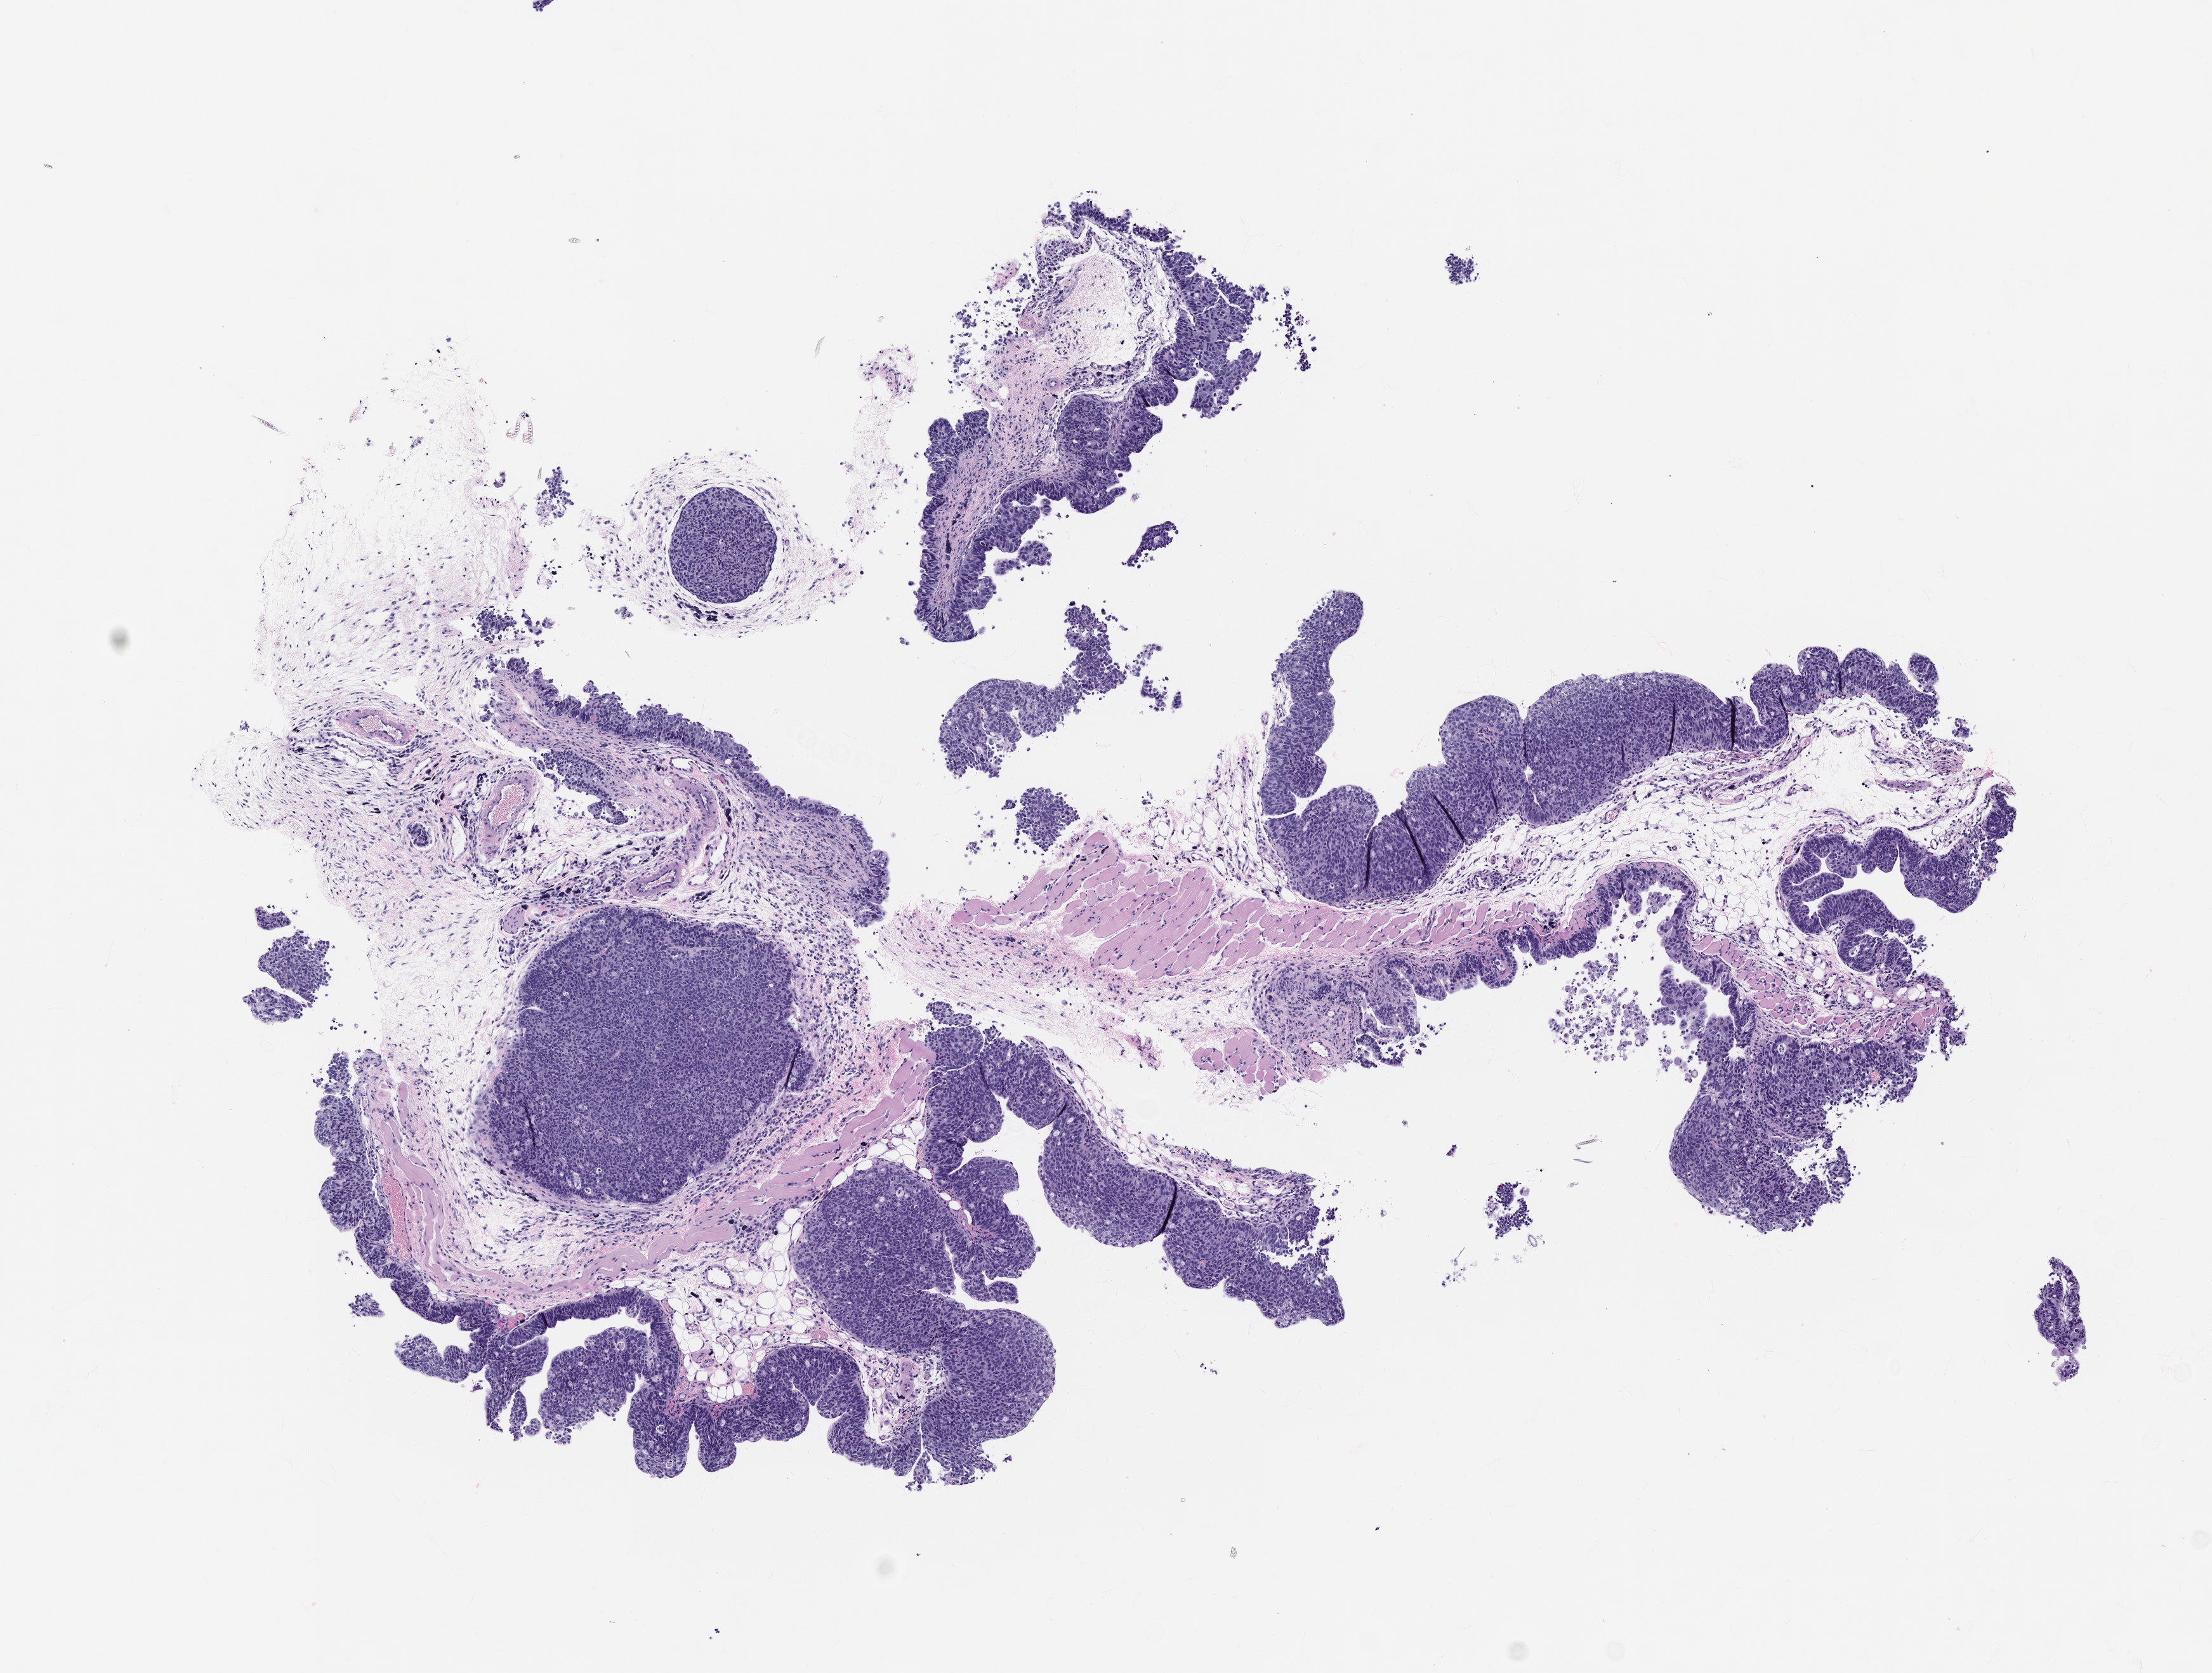
Whole-slide image, haematoxylin and eosin: patient-derived xenograft (human tumor grown in a mouse), passage 0, low-resolution overview of the scanned area, about 7.0 x 5.3 mm, FFPE section, tumor site category: gastrointestinal tract.
Originating patient diagnosis: Gastric Adenocarcinoma.